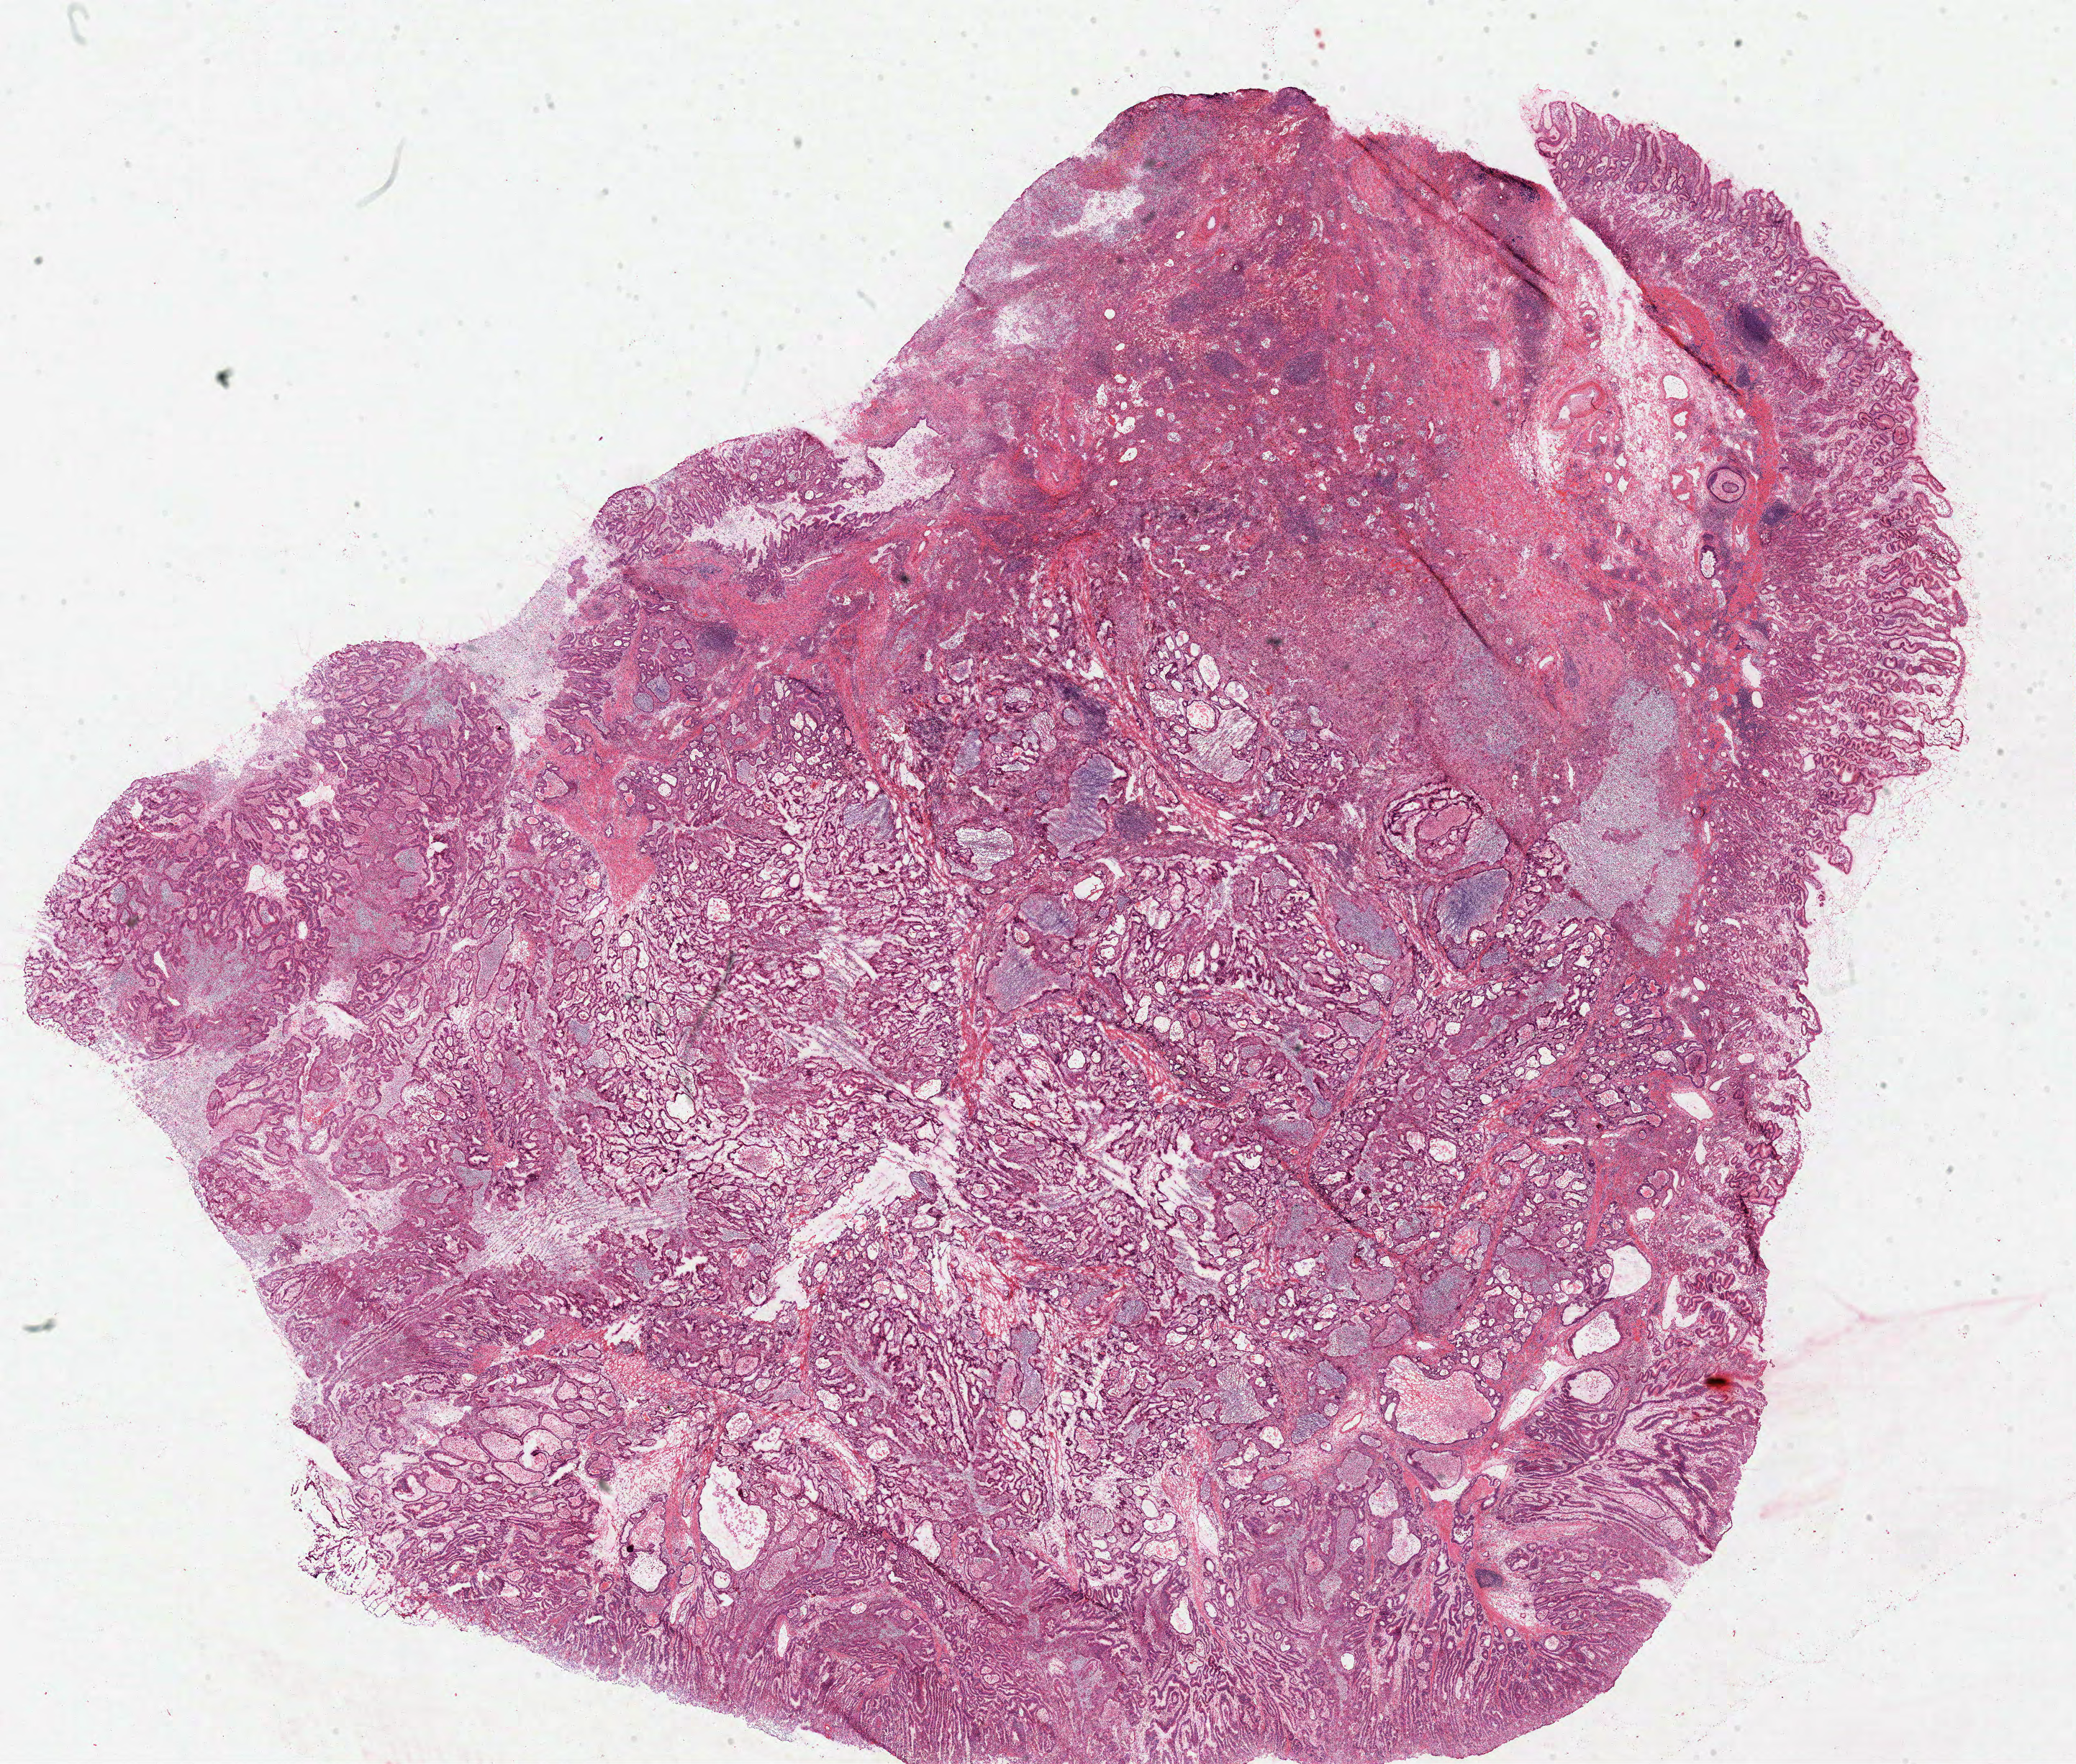
Whole-slide histology image, H&E-stained, low-resolution overview of the scanned area, about 22.7 x 19.3 mm; frozen section from the top of the tissue portion; sample: primary tumour, stomach. Patient: male, age at initial diagnosis 41 years. Histologic grade: G2 (moderately differentiated). Slide review estimates, as recorded: tumour cells 80%, tumour nuclei 60%, normal cells 10%, stromal cells 10%, necrosis 5%.
Pathologic diagnosis: Adenocarcinoma, NOS (cardia, NOS). AJCC pathologic stage: IB (7th edition). TNM: T2 N0 M0. Lymph nodes positive (case pathology): 0 of 15 examined.